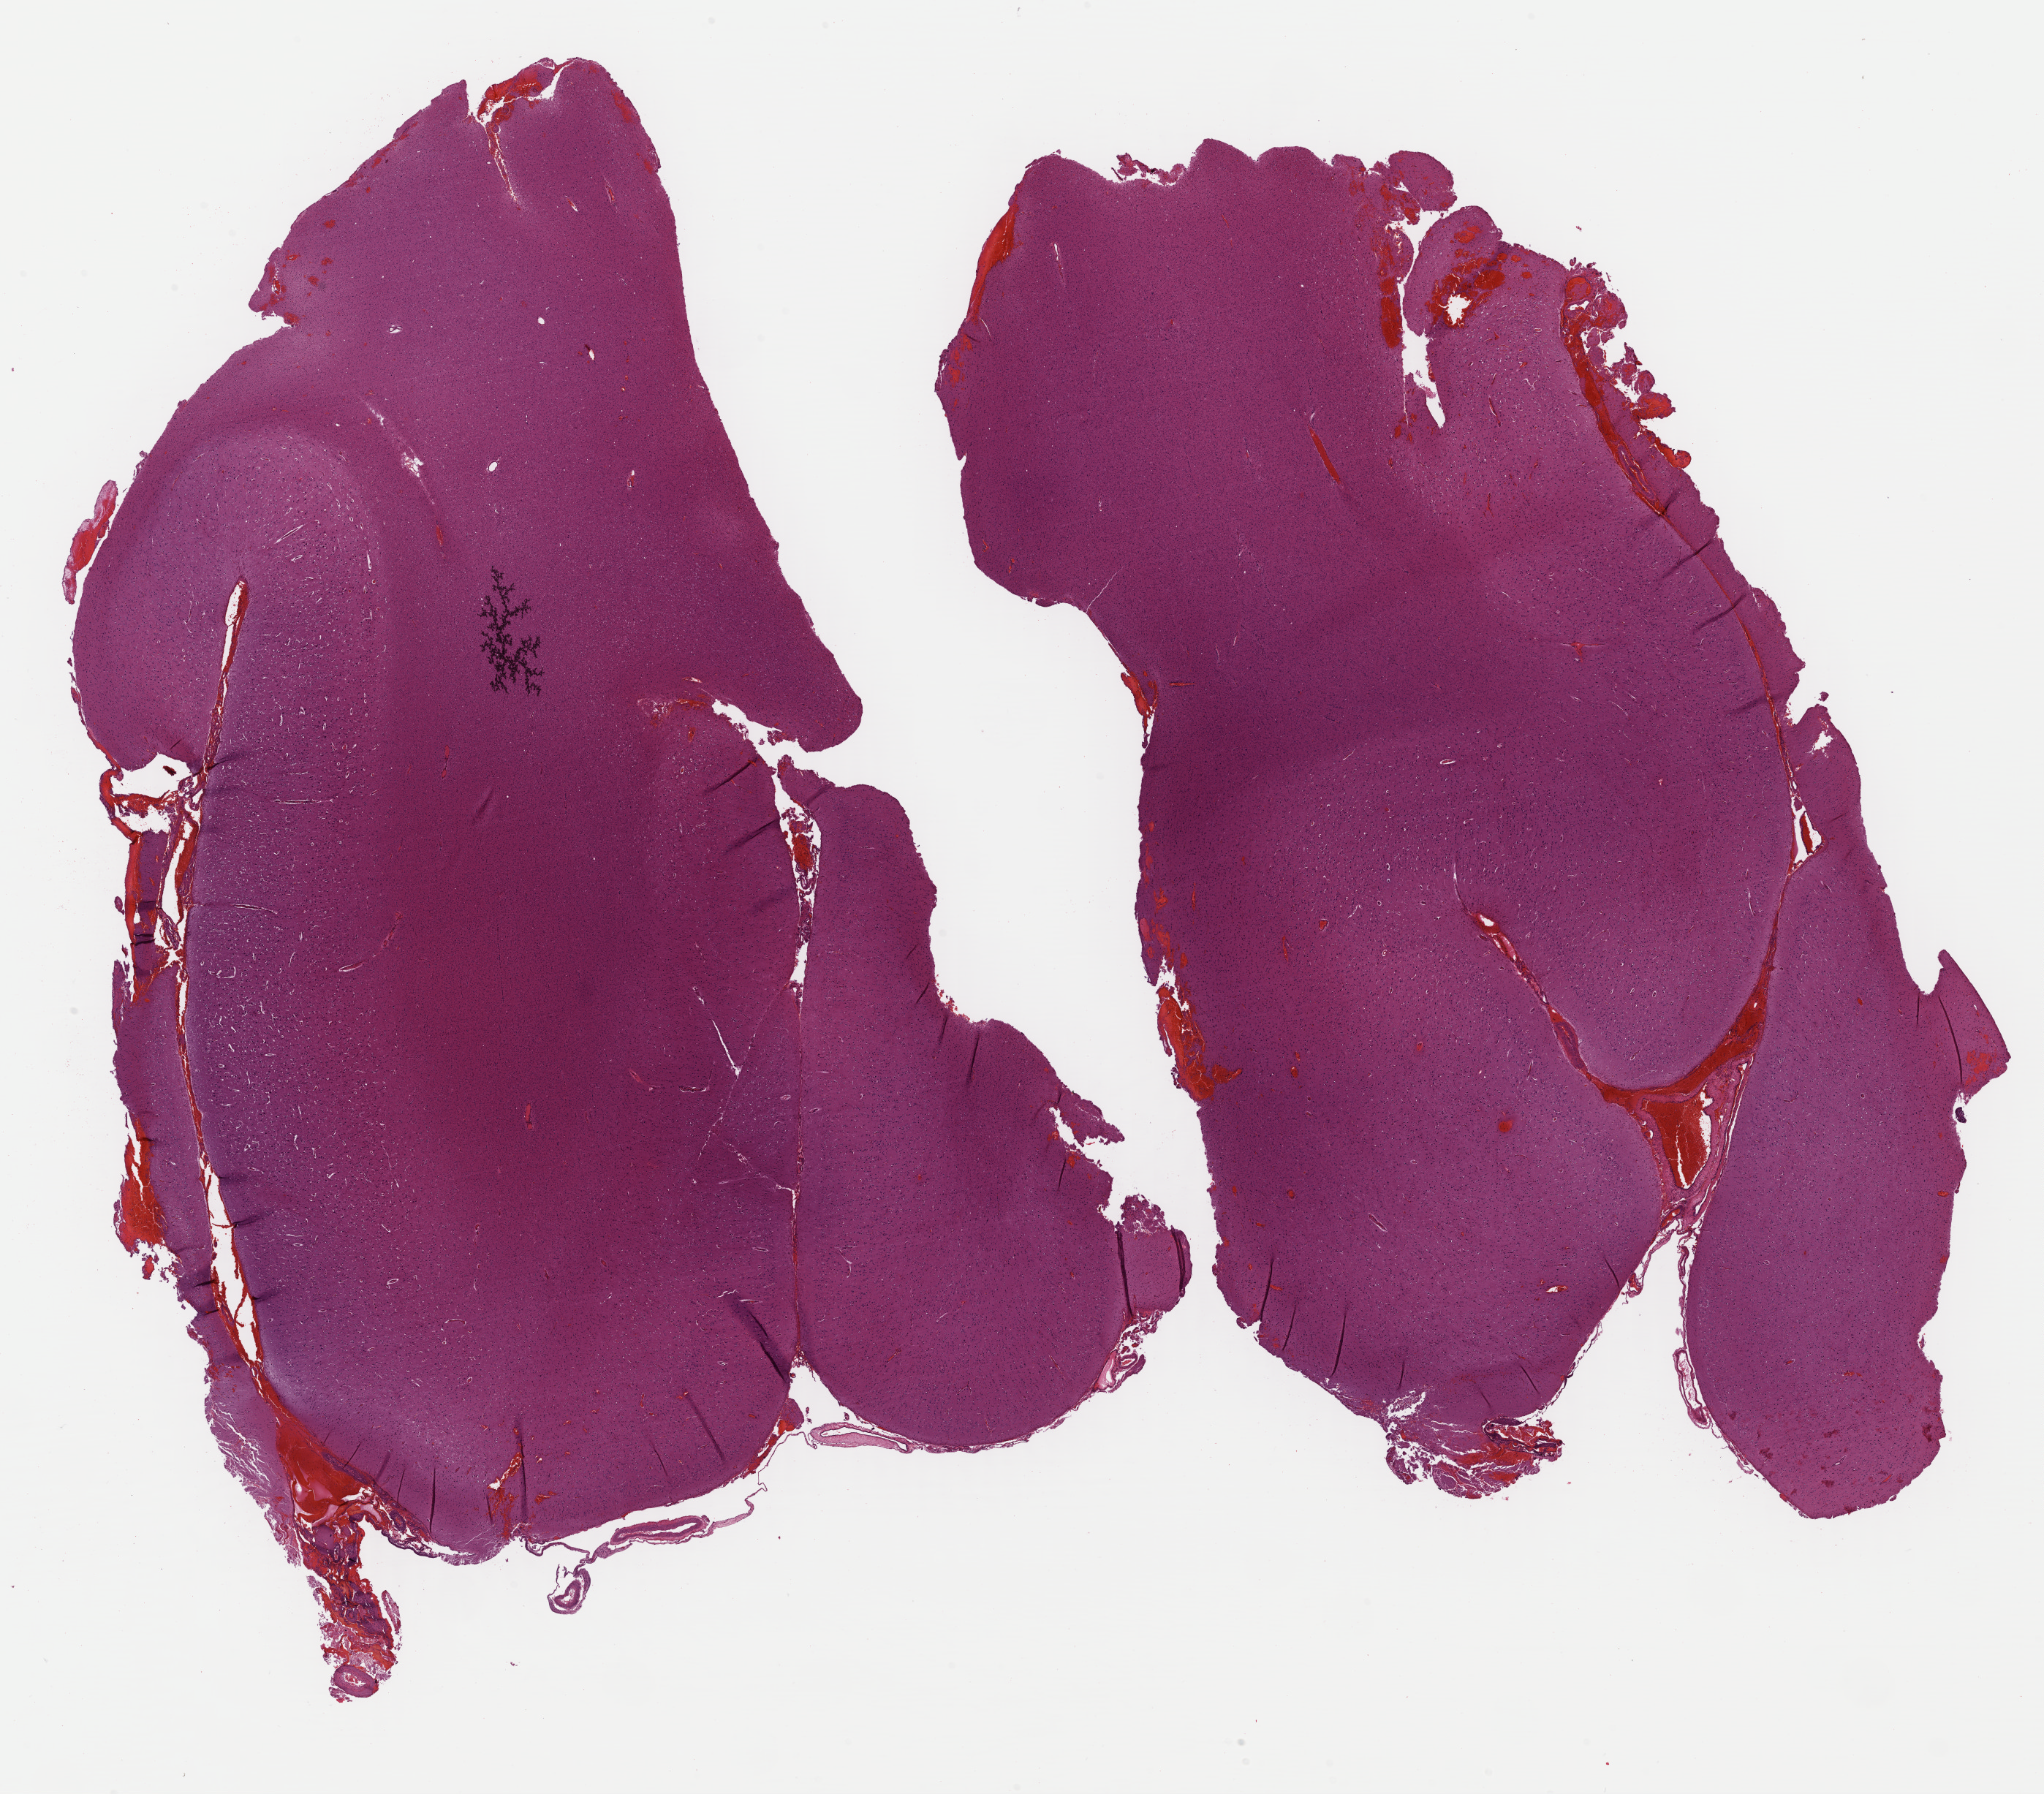
H&E-stained whole-slide image, whole scanned area (about 22.0 x 19.3 mm, from a 40x scan) shown as a low-resolution overview. FFPE section. Primary tumour sample from the brain. Female patient; age at initial diagnosis 61 years. Histologic grade: G2 (moderately differentiated).
Pathologic diagnosis: Astrocytoma, NOS (cerebrum). Laterality: left.